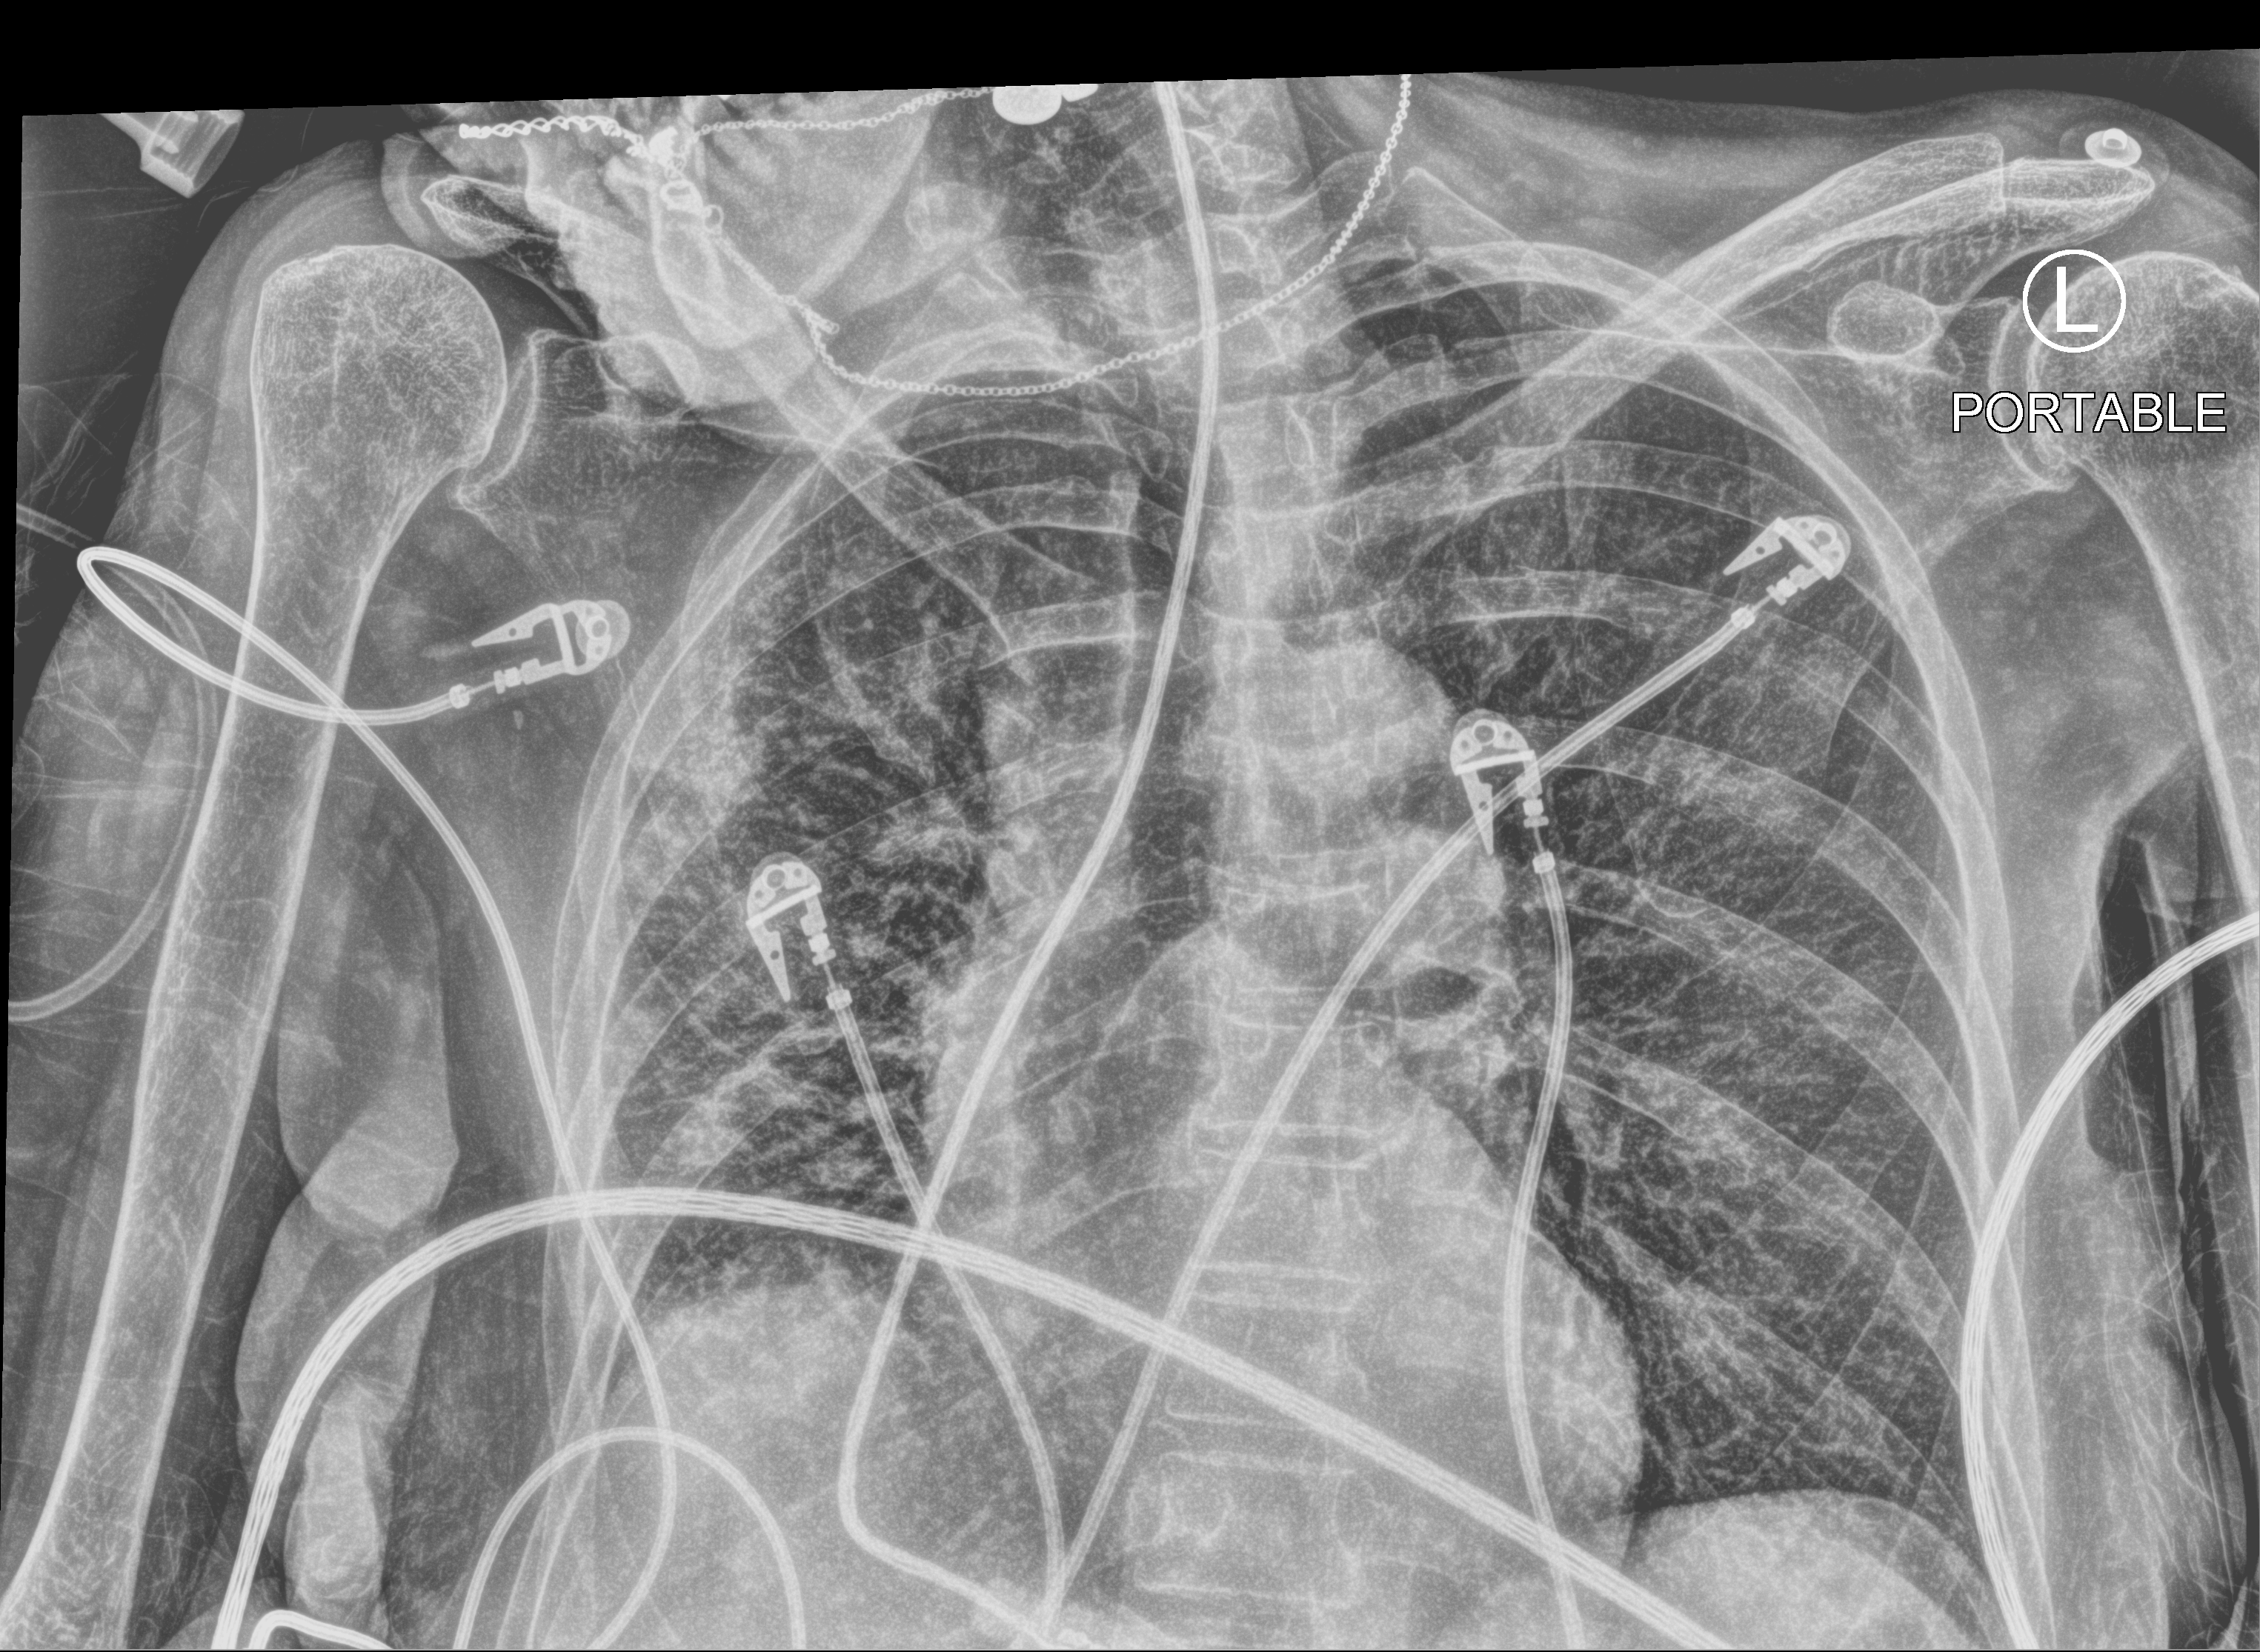
Chest X-ray (portable); anteroposterior (AP) projection. Female patient hospitalised with COVID-19, age 75–90 years.
Hospital-stay facts (about this admission, not read from this image; timing relative to this image not recorded):
- mechanically ventilated during this hospital stay: no
- admitted to intensive care during this hospital stay: no